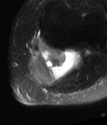
MRI of an extremity soft-tissue mass, one axial slice. Slice 48 of 78 in the series (ordered by position). T2-weighted fat-saturated. MR volume resampled by the dataset authors to the PET/CT grid (not the native acquisition matrix). 3.27 mm slice thickness. 107 × 125 image matrix, field of view 104 × 122 mm. Female patient. Case-level facts recorded for this patient, not image findings: histological type: extraskeletal high grade osteogenic sarcoma; grade: high; site of the primary tumour: left calf.
Outlined on this slice (expert contour drawn on MRI and transferred to this co-registered scan by the dataset authors):
- gross tumour volume (mass): box from (x=28, y=45) to (x=81, y=87) px